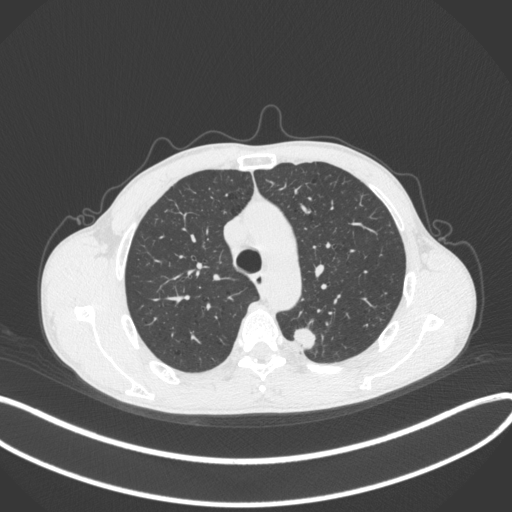
Chest CT, one axial slice; slice 291 of 429 in the series (ordered by position); 120 kVp; lung window (W 1500 / L -600 HU); 1 mm slice thickness; 512 × 512 image matrix, field of view 400 × 400 mm. Patient: male, 51 years. From the clinical record (not read from this slice): clinical TNM (as recorded): T2a N1 M1.
Annotated regions visible in this slice (bounding box drawn by a radiologist):
- lung tumour (recorded histology: adenocarcinoma): bounding box [x1, y1, x2, y2] px = [290, 325, 322, 355]